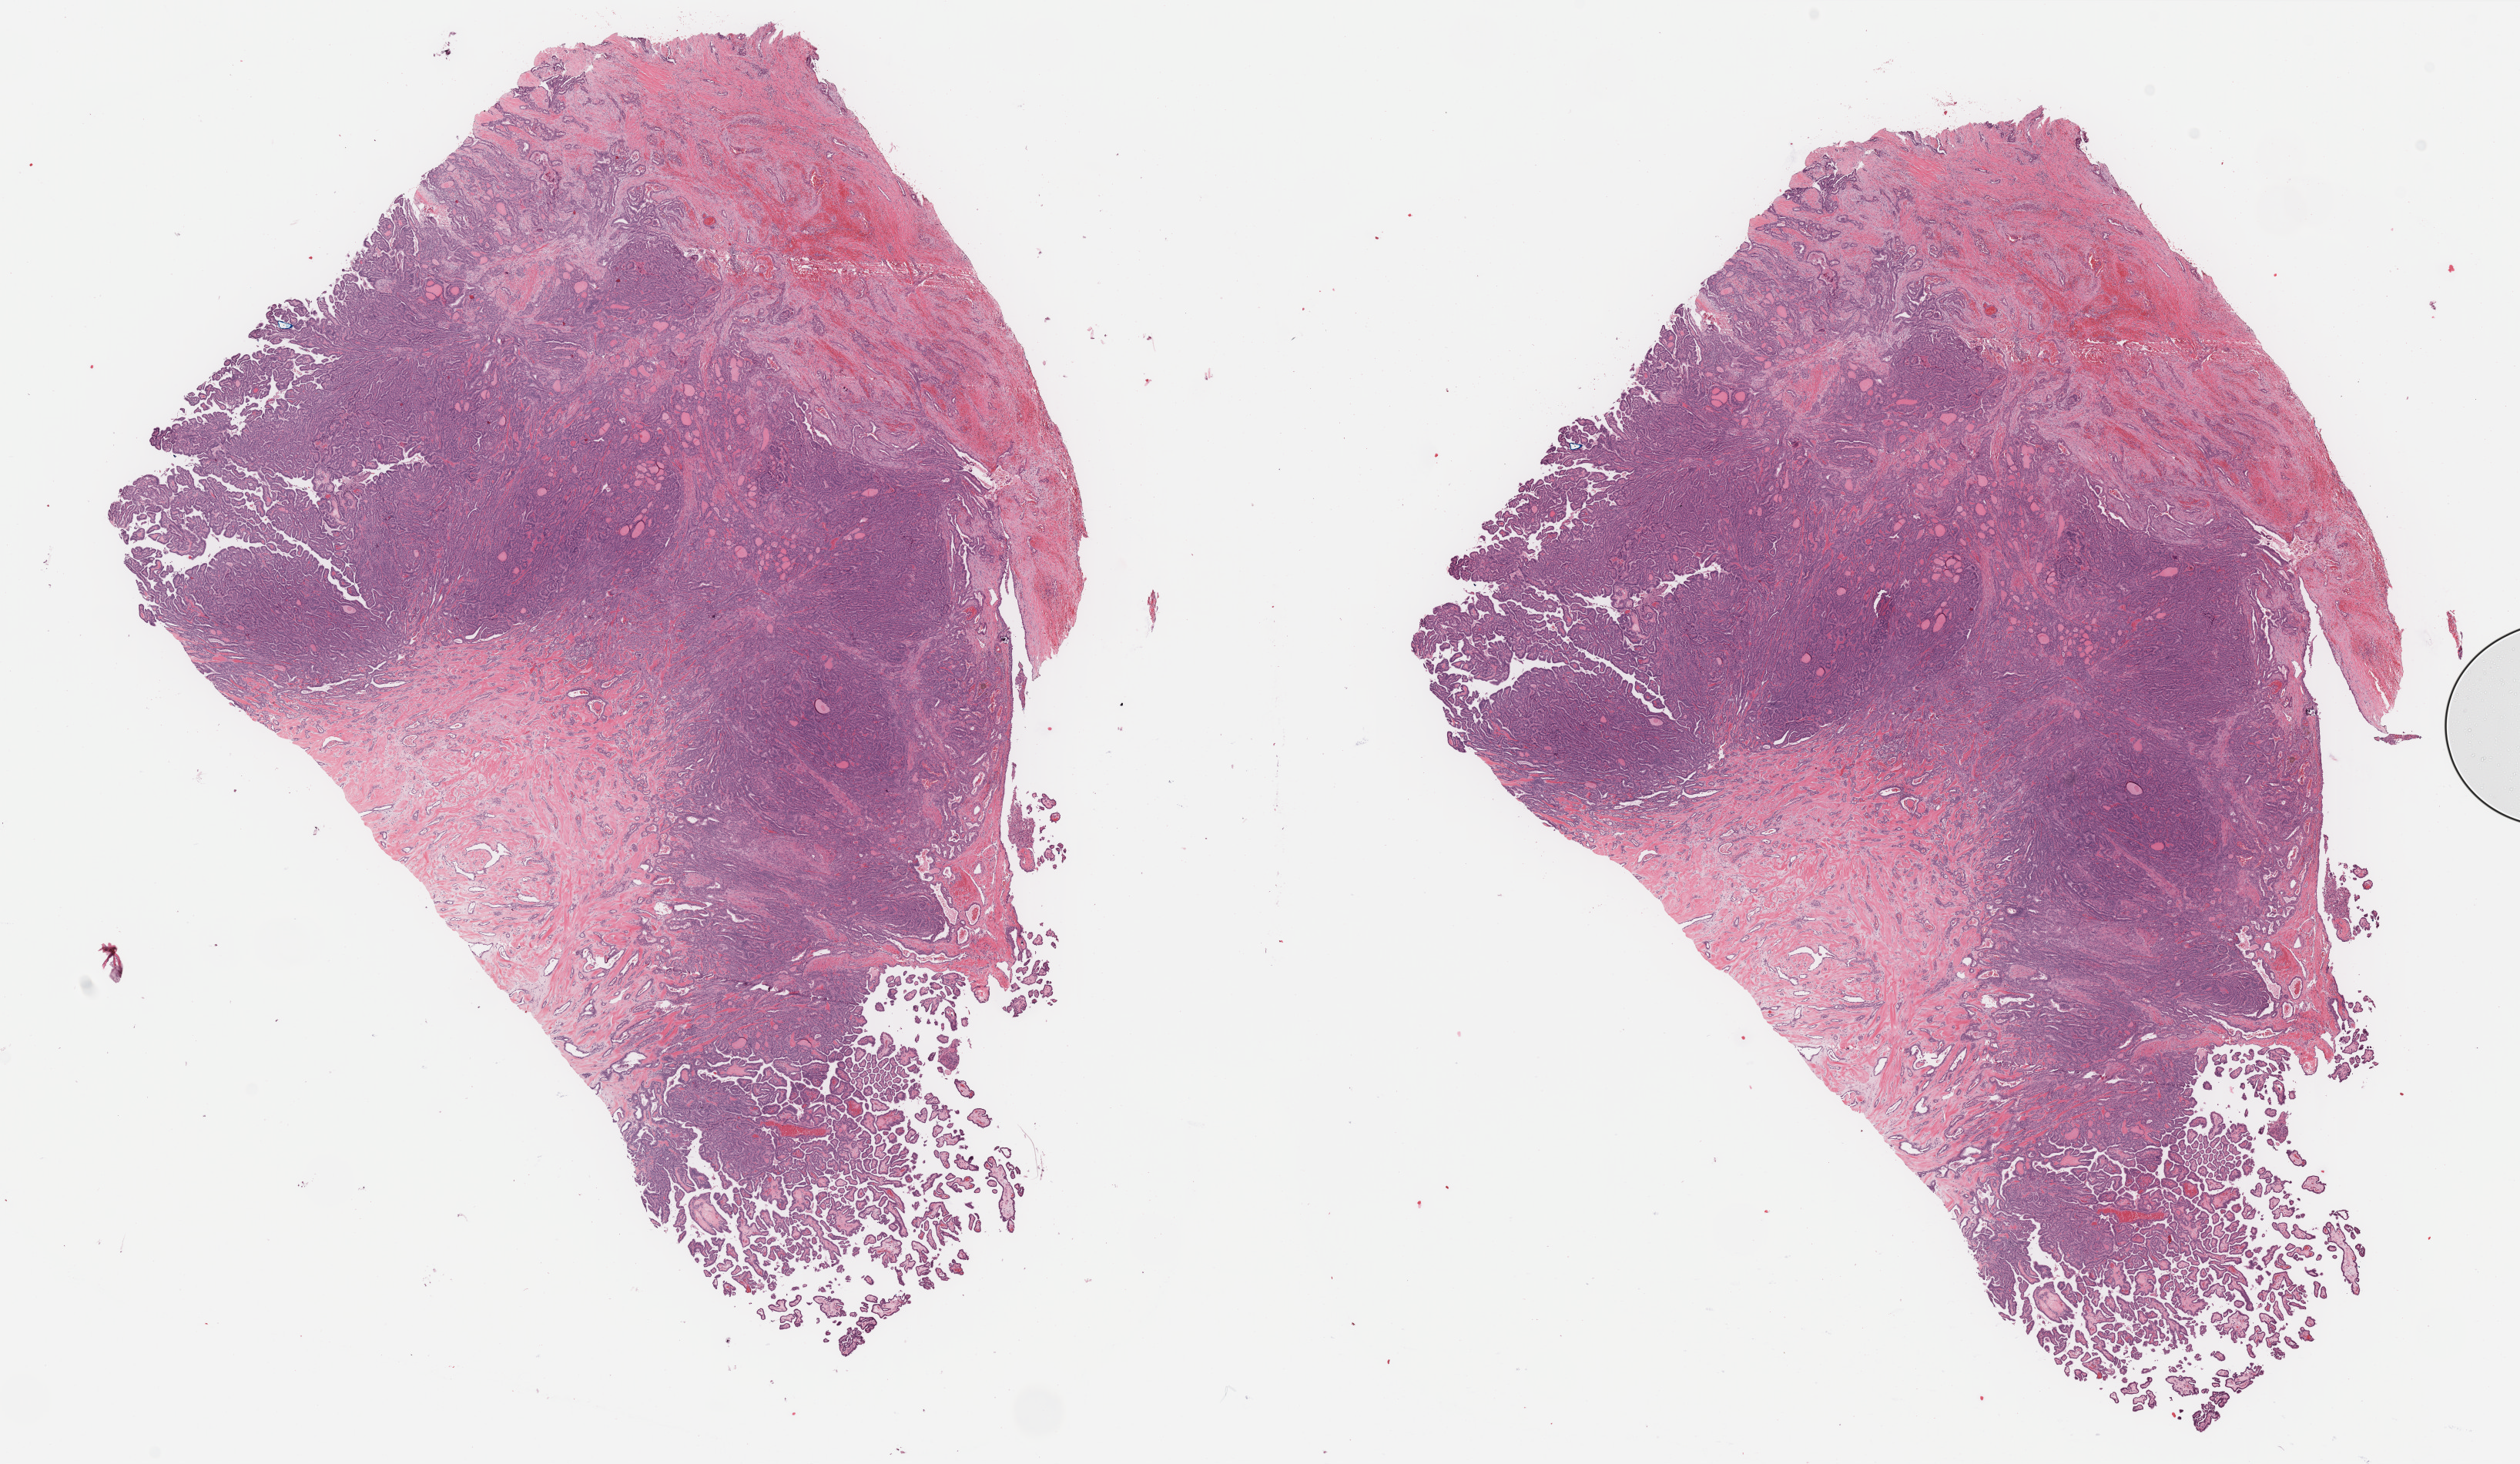
H&E-stained whole-slide image, low-resolution overview of the scanned area, about 25.9 x 15.0 mm; formalin-fixed paraffin-embedded (FFPE) diagnostic section; thyroid, primary tumour sample. Patient: female, age at initial diagnosis 52 years.
Lymph nodes positive (case pathology): 7 of 11 examined. AJCC pathologic stage: III. Histologic diagnosis: Papillary adenocarcinoma, NOS.